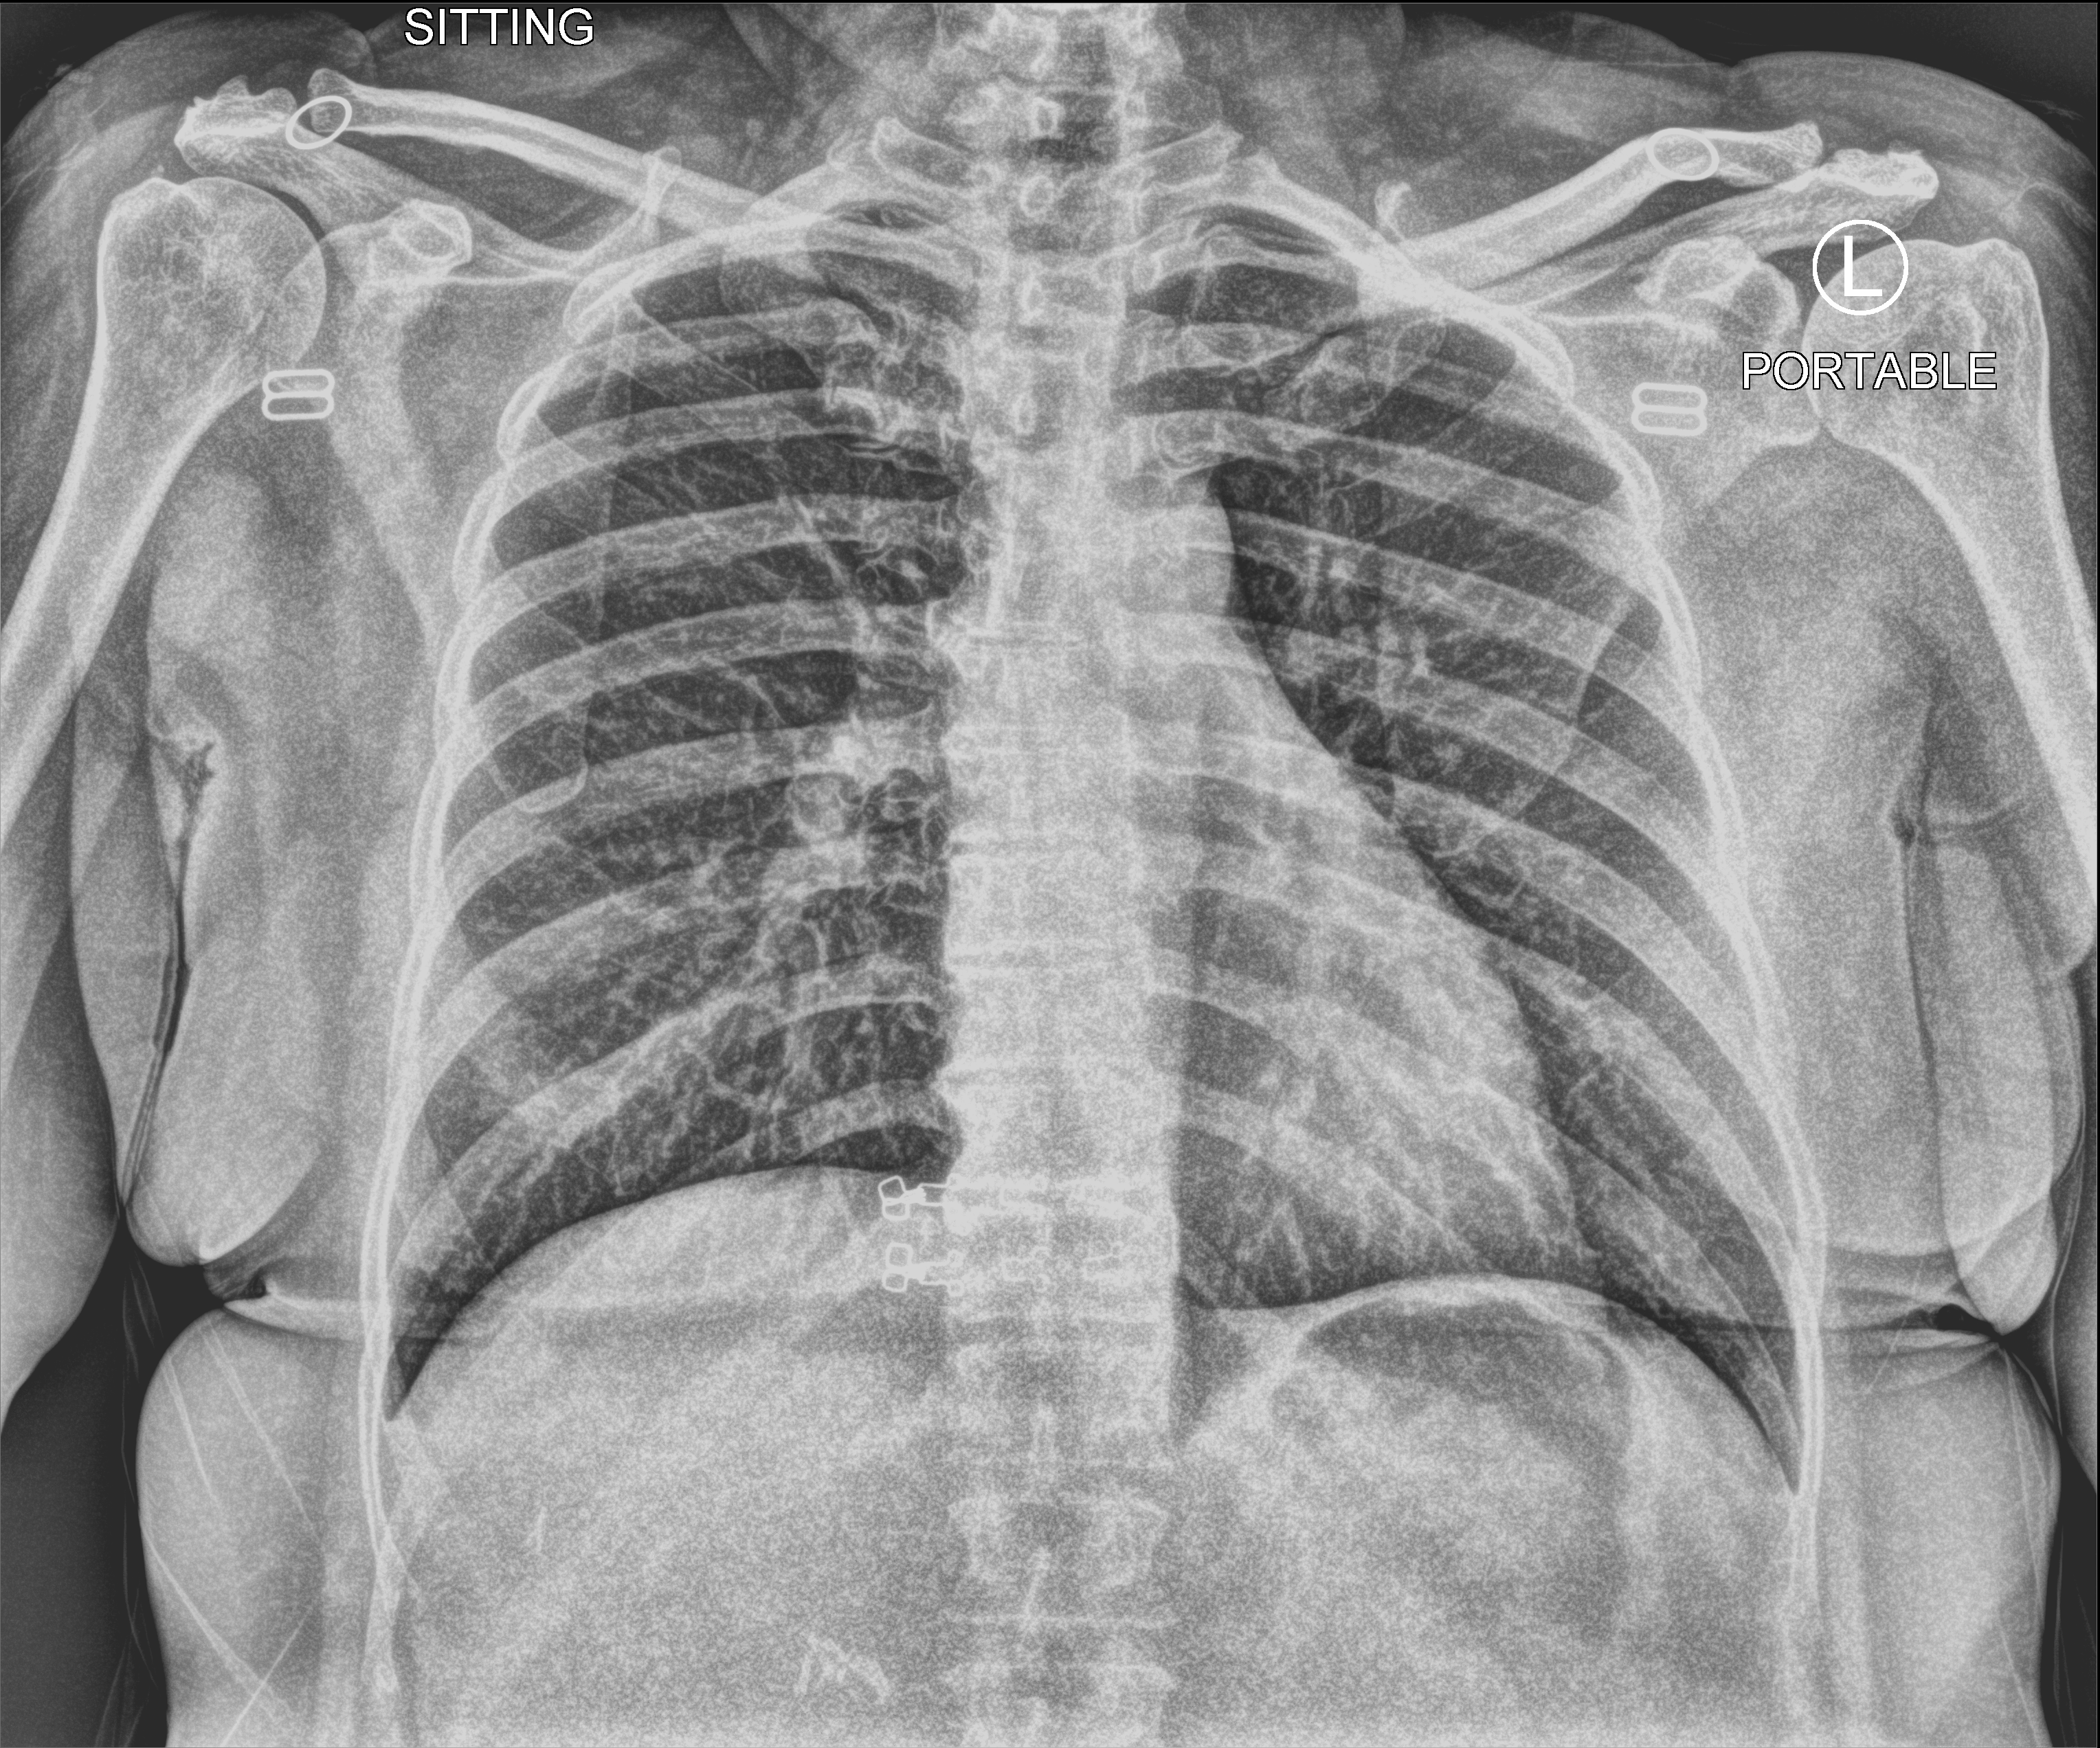
Bedside chest radiograph (computed radiography); anteroposterior (AP) projection. Patient hospitalised with COVID-19; female, aged 18–59 years.
Hospital-stay facts (about this admission, not read from this image; timing relative to this image not recorded):
- length of hospital stay: 1 day
- admitted to intensive care during this hospital stay: no
- mechanically ventilated during this hospital stay: no